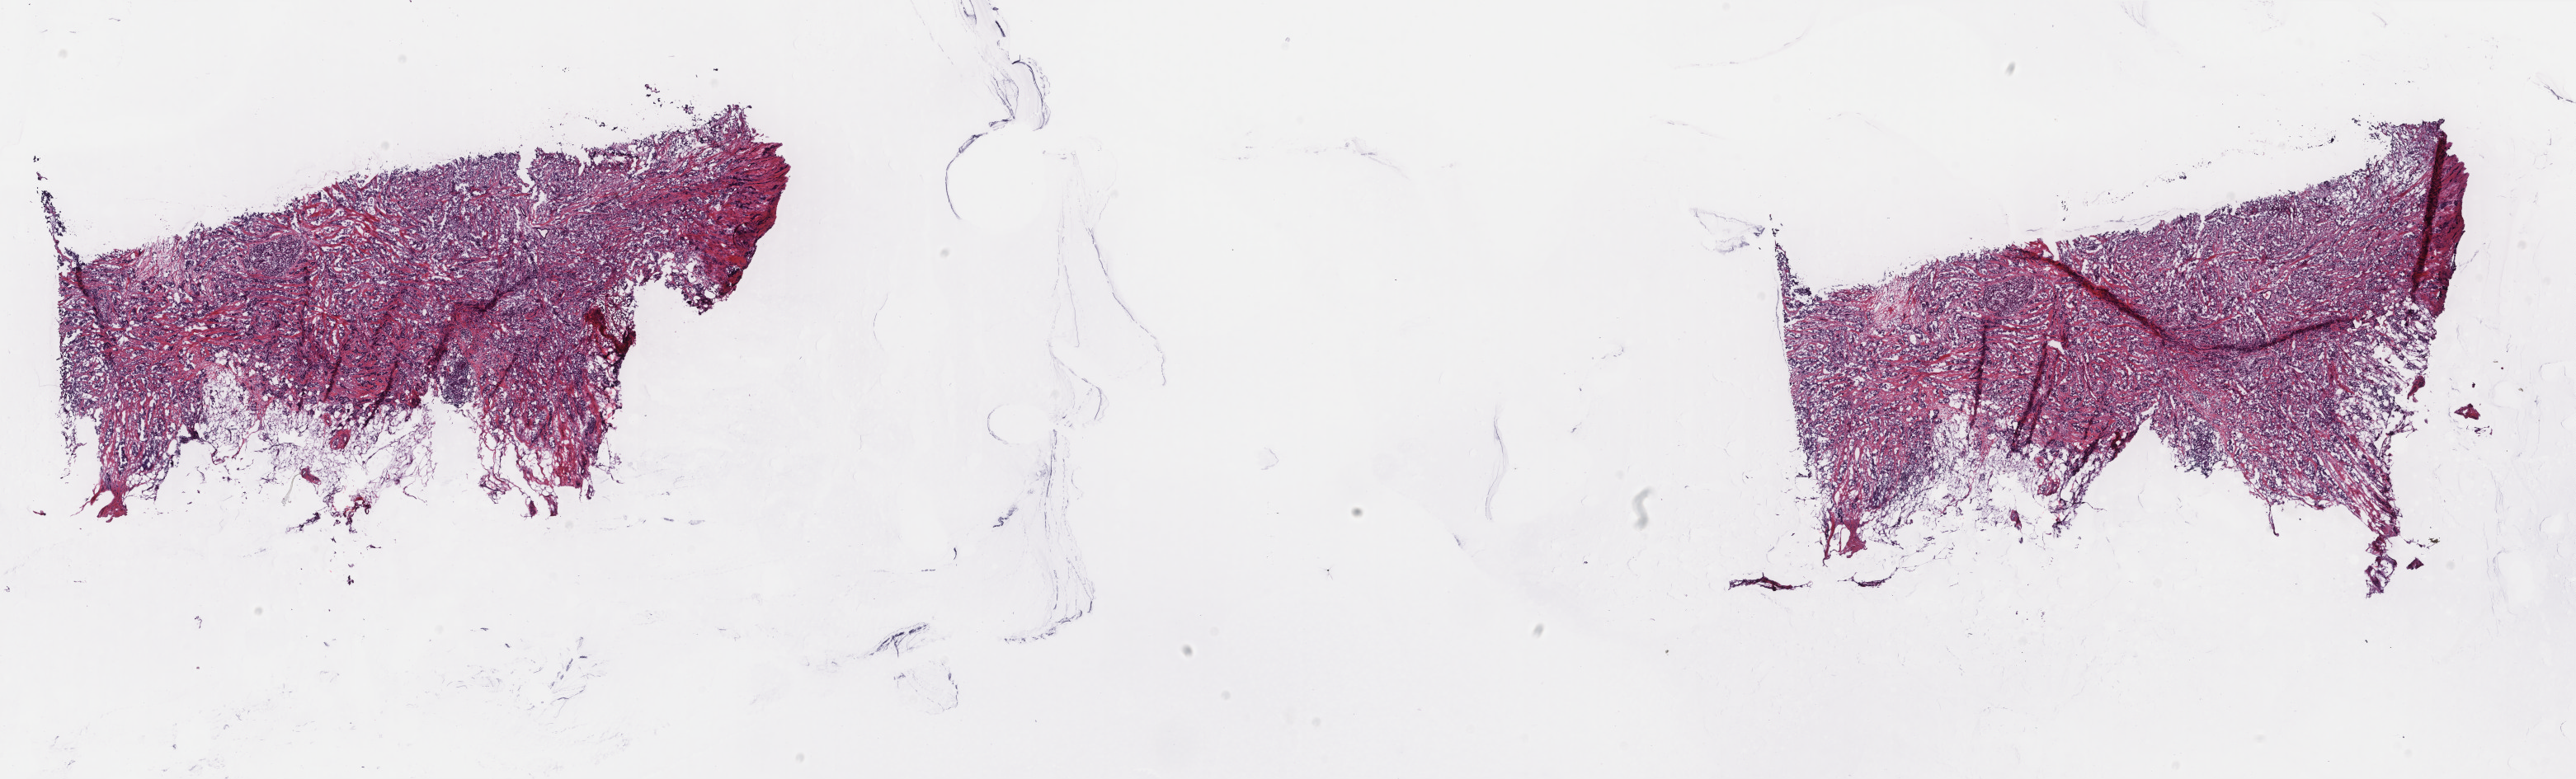
H&E whole-slide image — a low-resolution overview of the entire scanned area, about 24.8 x 7.5 mm (acquisition: 40x scan); frozen section; breast, primary tumour sample. Patient: female, age at initial diagnosis 52 years. Pathologist review of this section (percent, as recorded): tumour cells 65%, tumour nuclei 85%, normal cells 1%, stromal cells 34%, necrosis 0%. Infiltration values recorded for this section: lymphocyte infiltration 2%, monocyte infiltration 0%, neutrophil infiltration 0%.
Pathologic diagnosis: Infiltrating duct and lobular carcinoma. Lymph nodes positive (case pathology): 0 of 7 examined. AJCC pathologic stage: IIA (6th edition).